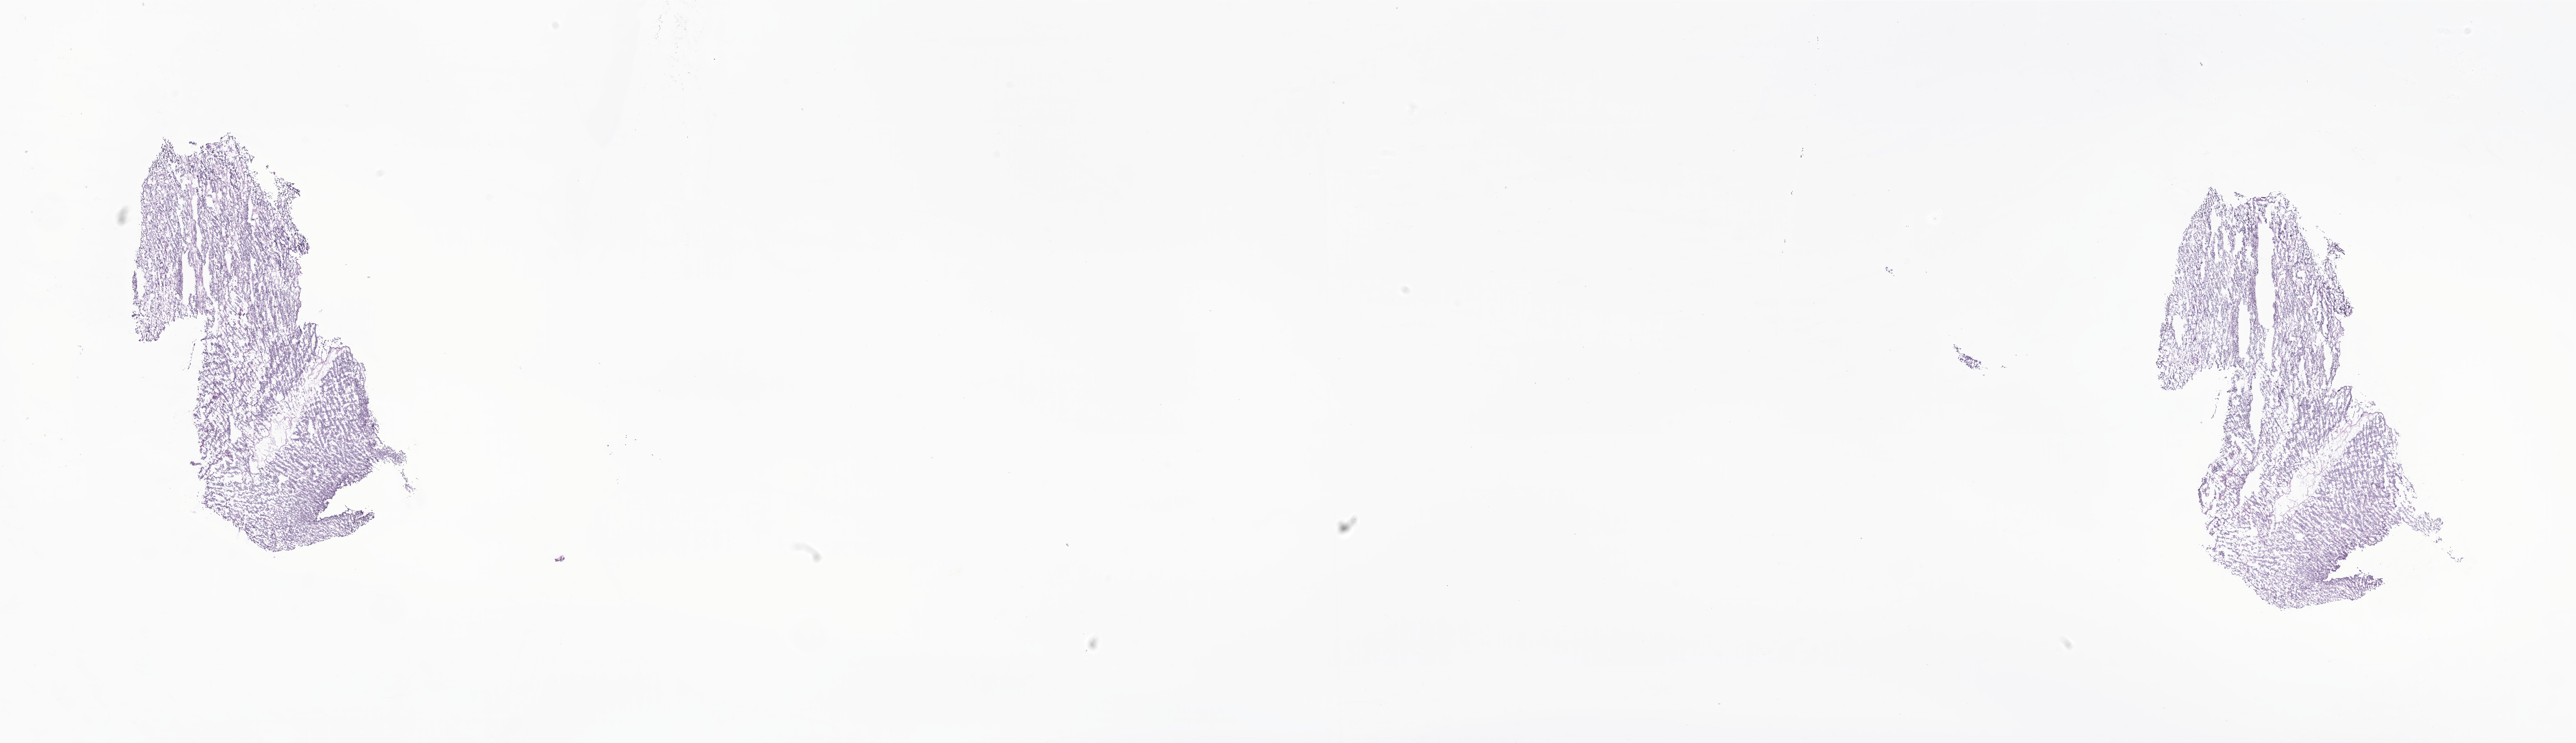
Whole-slide image, hematoxylin and eosin (H&E) stain of tumor tissue from the central nervous system, a low-resolution overview of the entire scanned area, about 35.5 x 10.2 mm; frozen section (OCT-embedded). Patient male; age 58 months (4 years 10 months).
Diagnosis (ICD-O-3 morphology term): Neoplasm, malignant.